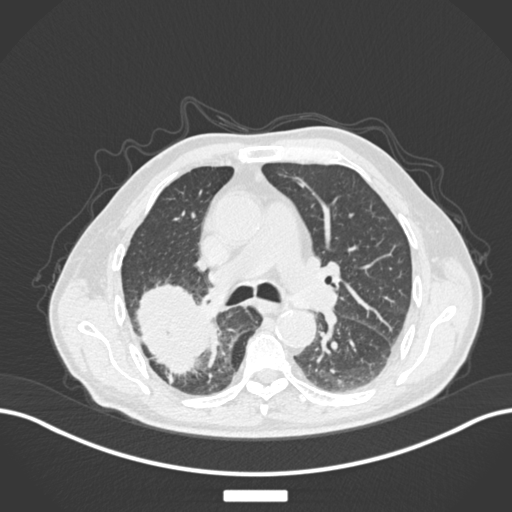
Chest CT, one axial slice; position 106 of 201 along the scan axis; reconstruction kernel B30f; 120 kVp; lung window (W 1500 / L -600 HU); 1 mm slice thickness; 512 × 512 image matrix, field of view 400 × 400 mm. Male patient, age 72 years. From the clinical record (not read from this slice): clinical TNM (as recorded): T3 N2 M0.
Outlined on this slice (rectangle marked by the reading radiologist):
- lung tumour (recorded histology: adenocarcinoma): box from (x=133, y=283) to (x=214, y=379) px